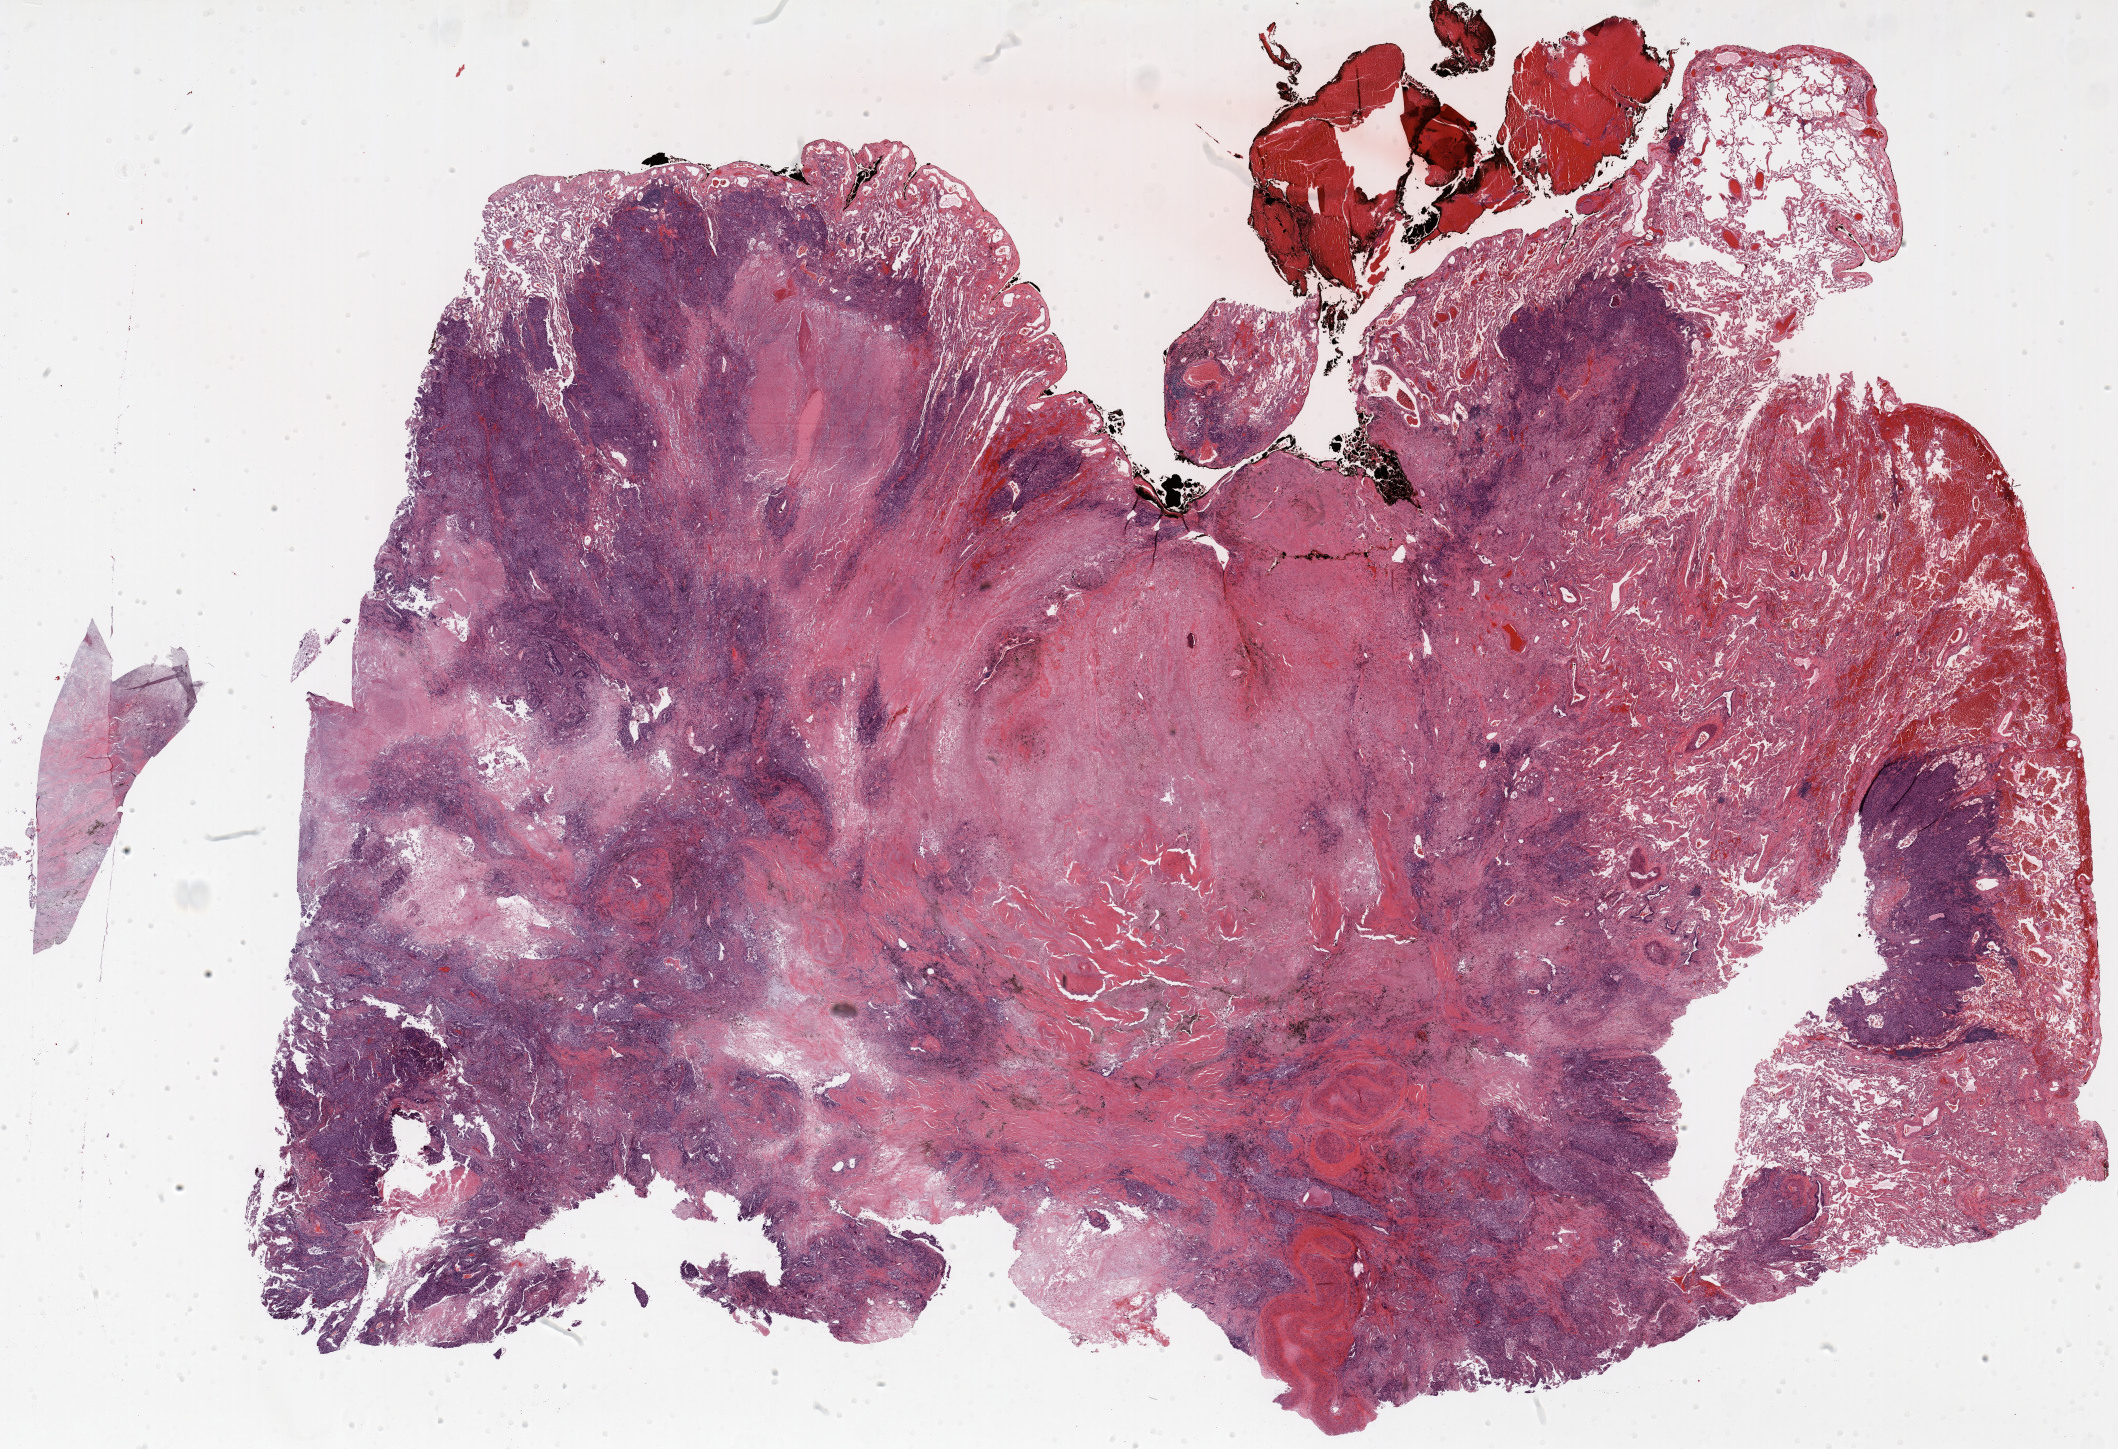
Whole-slide histology image, Hematoxylin and eosin (H&E) stained, whole scanned area (about 34.0 x 23.3 mm) shown as a low-resolution overview. Formalin-fixed paraffin-embedded (FFPE) section. Lung. Male patient, aged 69 at enrolment. Current smoker at enrolment. Grade: poorly differentiated (G3).
Tumour size (pathology): 40 mm. Primary tumour location (clinical record): right upper lobe. Stage (AJCC 6th edition): IB. Participant's lung-cancer diagnosis: Adenocarcinoma, NOS (ICD-O-3 8140/3).